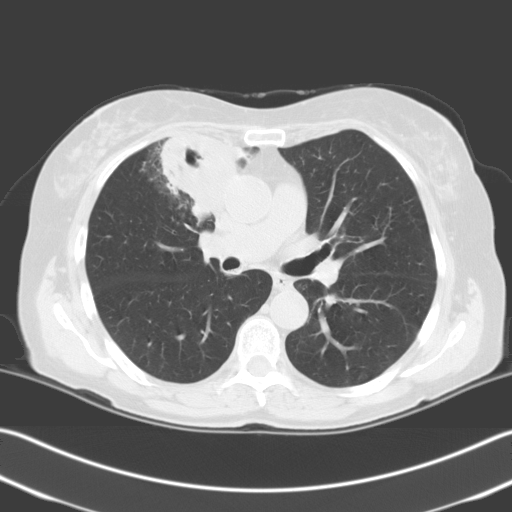
Low-dose screening chest CT, one axial slice; position 128 of 204 along the scan axis; 140 kVp; lung window (W 1500 / L -600 HU); 3.2 mm slice thickness; 512 × 512 image matrix, field of view 348 × 348 mm.
Structures marked on this image (expert manual segmentation):
- lesion 1 (tumor, upper lobe of right lung): box from (x=160, y=133) to (x=251, y=221) px